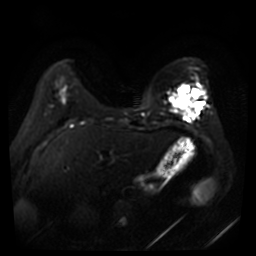
Breast MRI, one axial slice; diffusion-weighted series; image 2 of 4 stored at this slice position (different b-values; order by instance number); 3 T; 5 mm slice thickness; 256 × 256 image matrix, field of view 360 × 360 mm. Female patient.
Outlined on this slice (outlined manually by an expert reader):
- tumour on diffusion-weighted imaging: box from (x=171, y=95) to (x=188, y=113) px